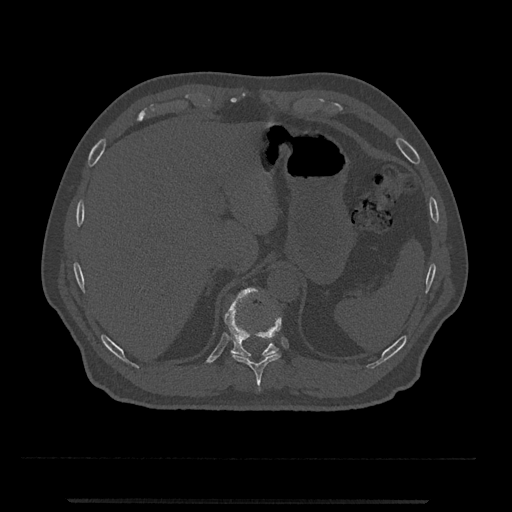
CT including the spine, one axial slice. Position 494 of 797 along the scan axis. Reconstruction kernel Br40s/3. 120 kVp. Bone window (W 1800 / L 400 HU). 0.5 mm slice thickness. 512 × 512 image matrix, field of view 419 × 419 mm. Male patient, age 63 years. Case-level facts recorded for this patient, not image findings: primary cancer: prostate.
Annotated regions visible in this slice (semi-automatic segmentation, software-assisted and operator-edited):
- T10 vertebra: bounding box (x1, y1, x2, y2) in pixels: (232, 317, 282, 391)
- T11 vertebra: (225, 287, 279, 356)